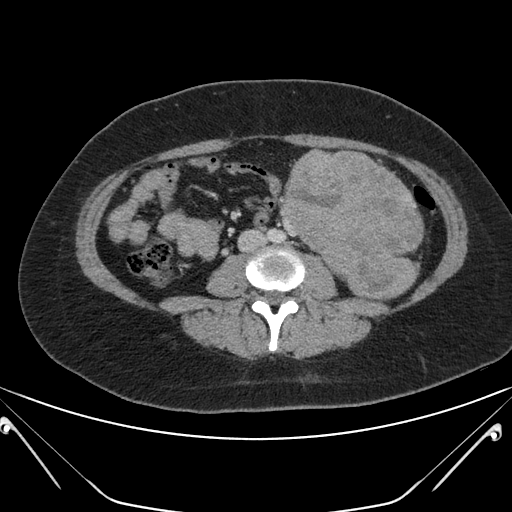
Contrast-enhanced abdominal CT, one axial slice. Position 86 of 168 along the scan axis. Soft-tissue window (W 400 / L 40 HU). 3 mm slice thickness. 512 × 512 image matrix, field of view 394 × 394 mm. Patient: female, 26 years. Case-level facts recorded for this patient, not image findings: diagnosis: adrenocortical carcinoma; tumour side: left adrenal; tumour size at pathology: 28 cm; Ki-67 index: 20 %; stage (as recorded): 2.
Structures marked on this image (semi-automatically segmented with operator editing):
- mass: box from (x=283, y=150) to (x=423, y=298) px